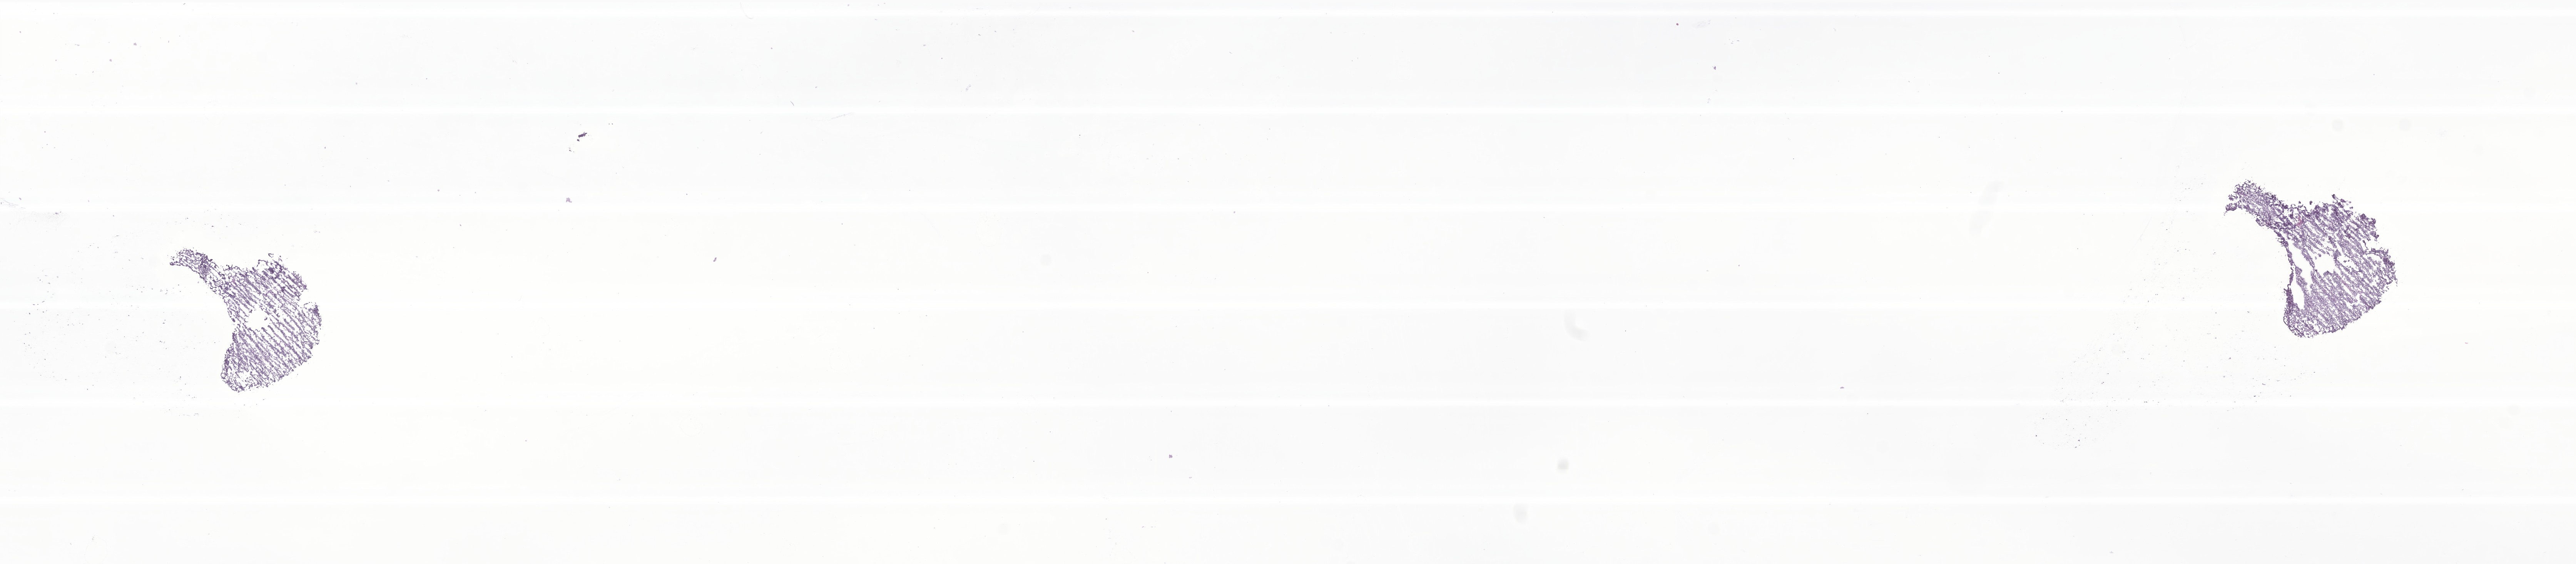
Whole-slide image, H&E stain of tumor tissue from the brain — shown as a low-resolution overview of the whole scanned area (about 28.2 x 6.2 mm); frozen section. Female patient, age 722 days (about 2.0 years).
Recorded diagnosis: Neoplasm, uncertain whether benign or malignant.